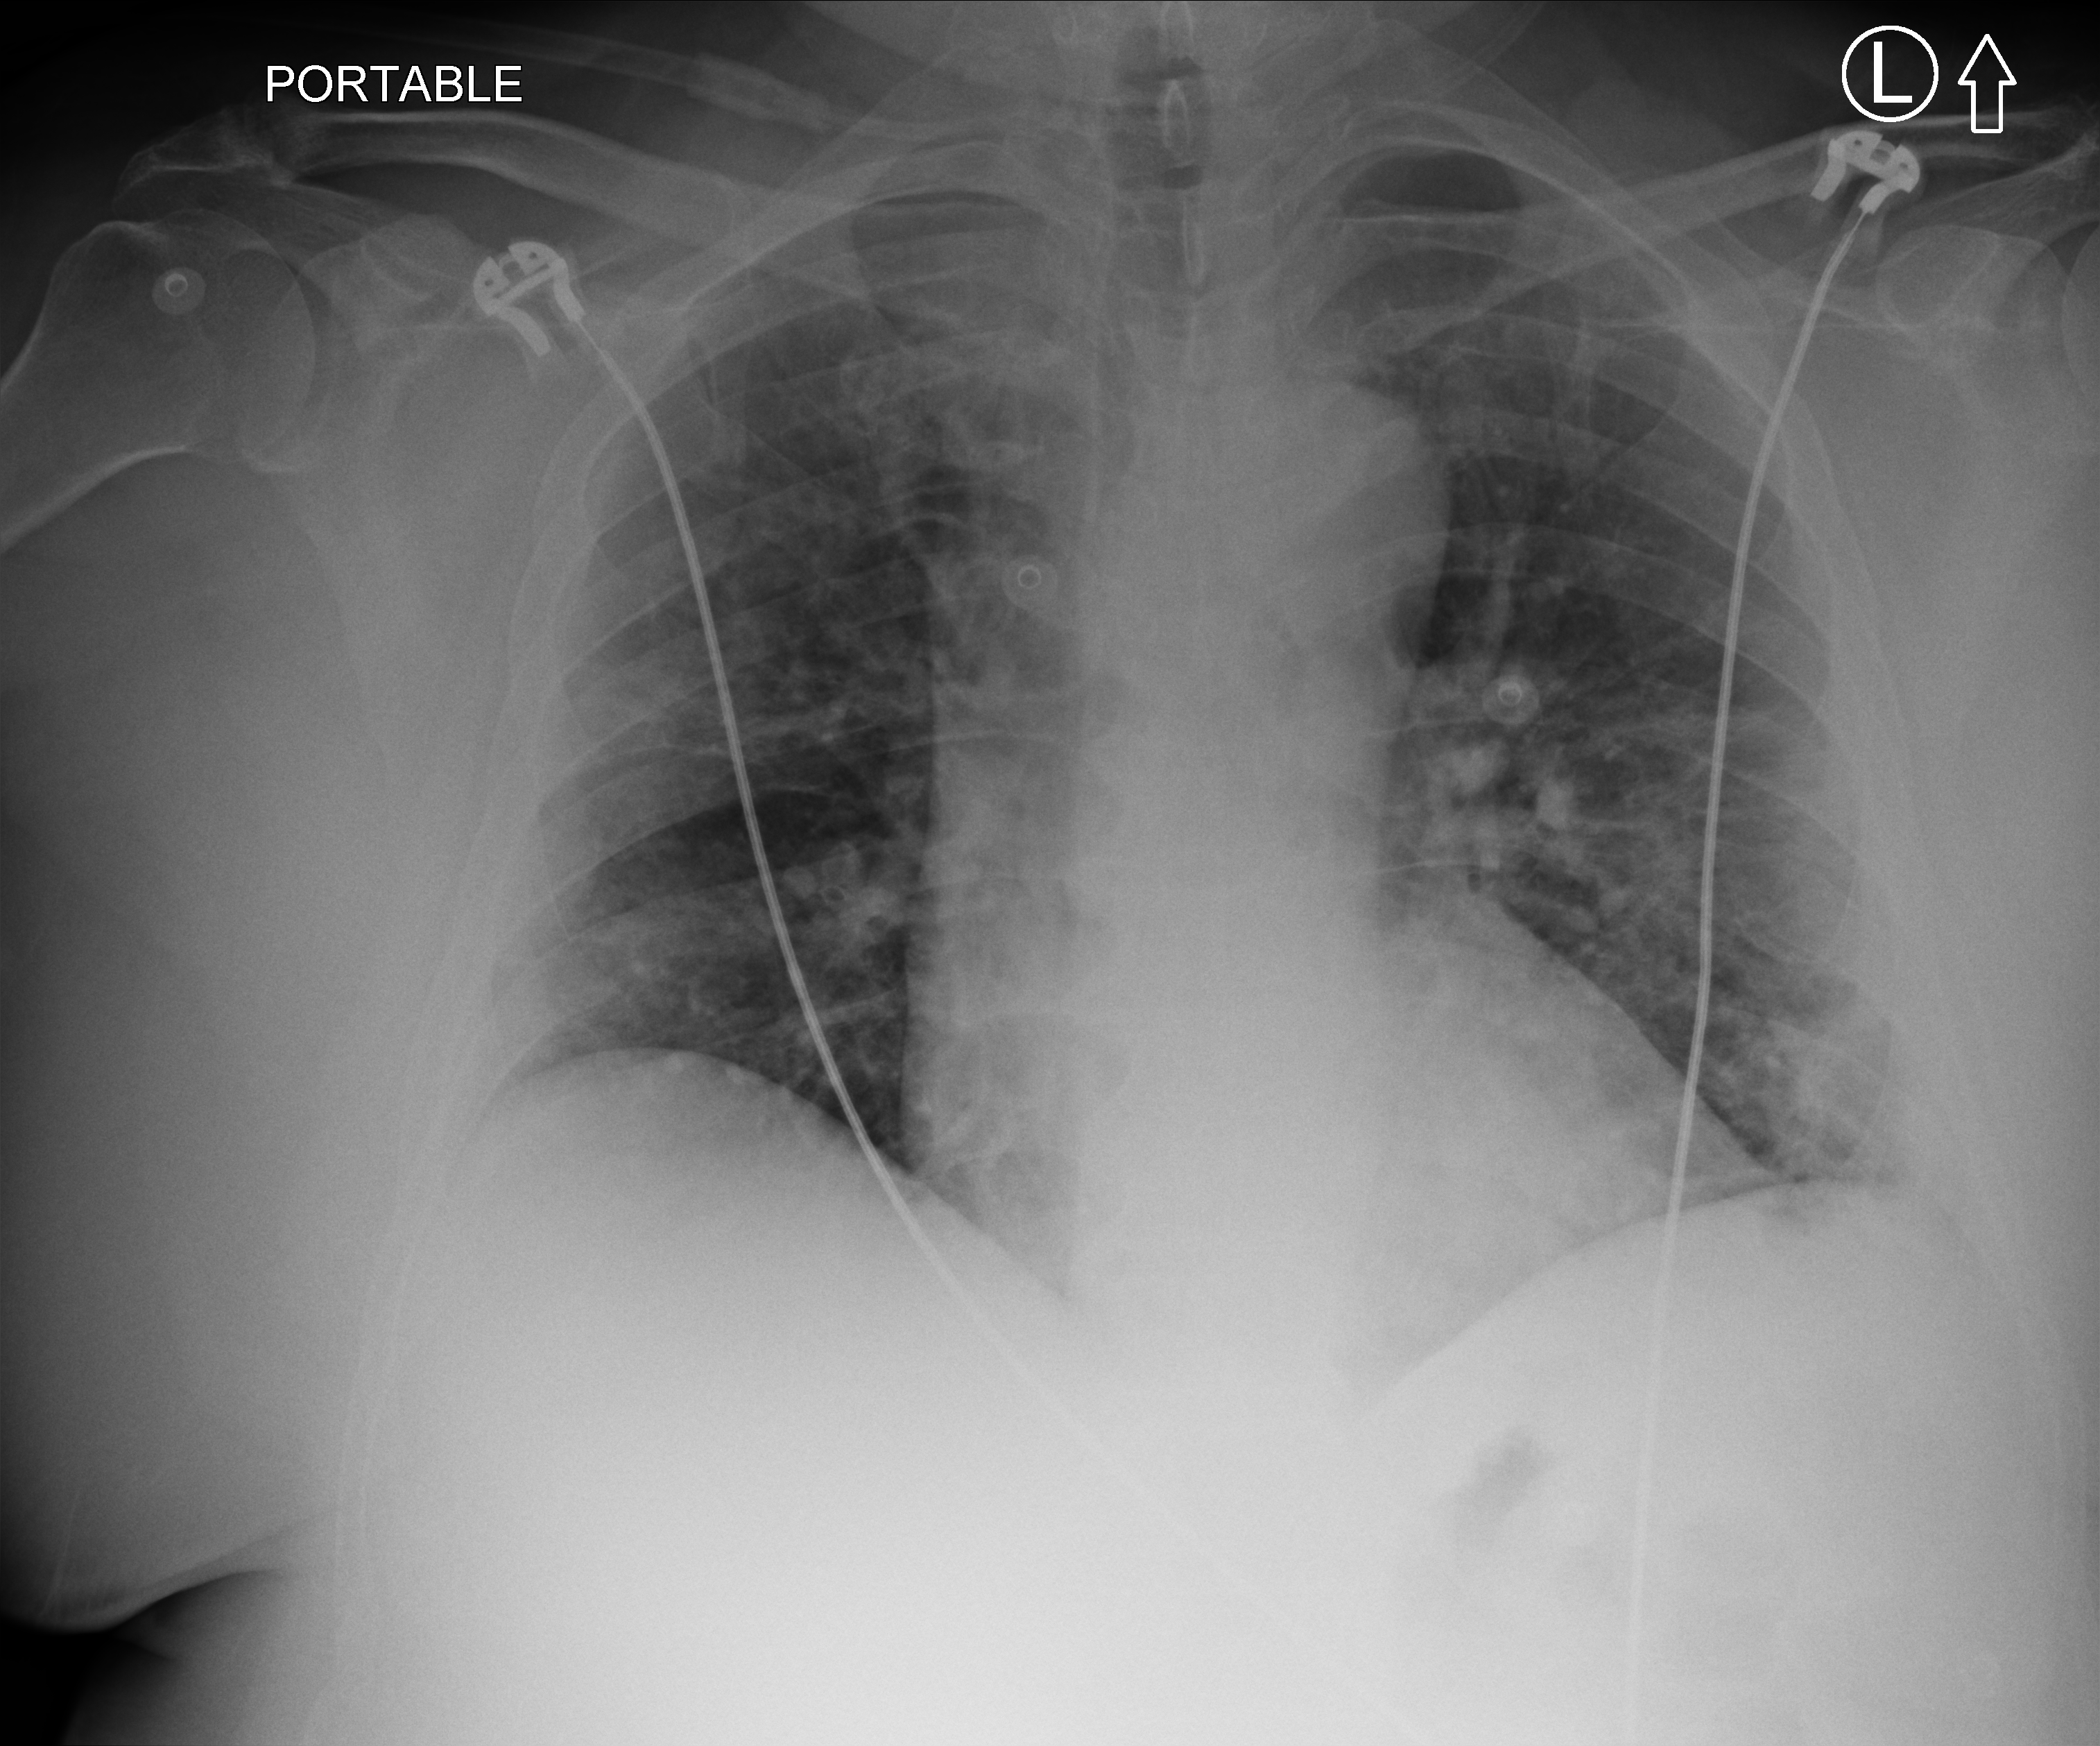
Portable chest radiograph; anteroposterior (AP) projection. Patient hospitalised with COVID-19, aged 18–59 years.
From the hospital-stay record, not from the radiograph (when in the stay this image was taken is not recorded):
- mechanically ventilated during this hospital stay: yes
- diabetes (admission record): no
- admitted to intensive care during this hospital stay: yes